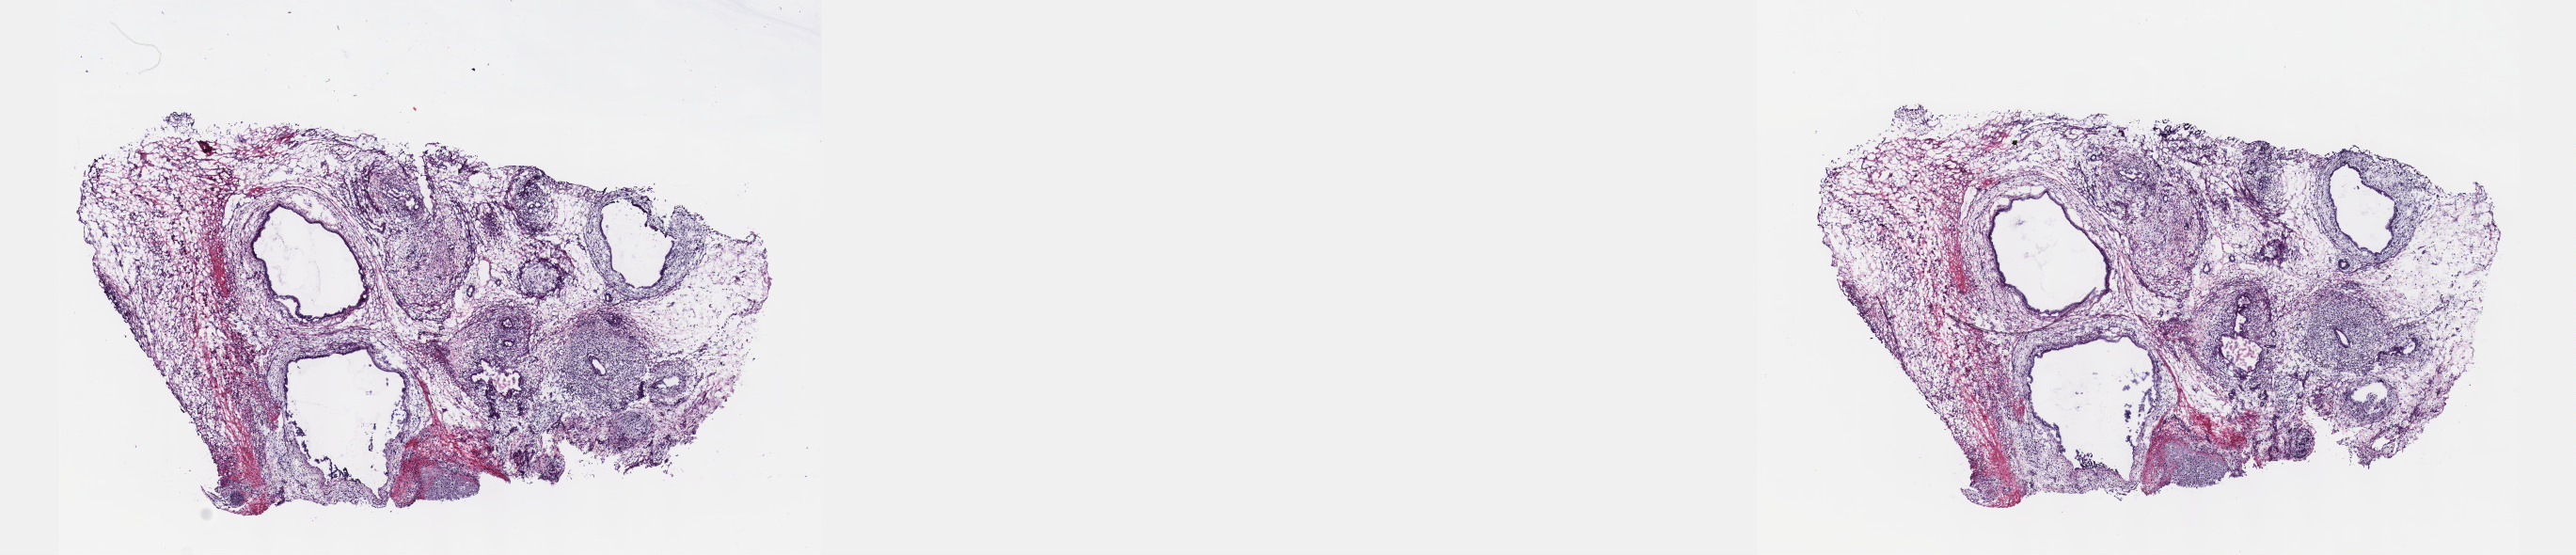
Digitized Hematoxylin and eosin (H&E) stained tissue section (whole slide), a low-resolution overview of the entire scanned area, about 22.1 x 4.8 mm; frozen section from the top of the tissue portion; primary tumour sample from the testis. Patient: male, age at initial diagnosis 30 years. Slide review estimates, as recorded: tumour cells 95%, tumour nuclei 95%, normal cells 0%, stromal cells 5%, necrosis 0%. Infiltration values recorded for this section: lymphocyte infiltration 0%, monocyte infiltration 0%, neutrophil infiltration 0%.
- AJCC pathologic stage: IS (7th edition)
- histologic diagnosis: Mixed germ cell tumor
- TNM: T2 NX M0